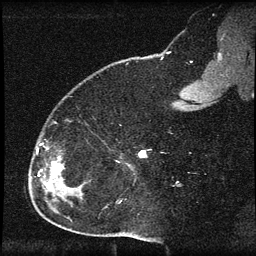
Breast MRI (dynamic contrast-enhanced), one sagittal slice; slice 19 of 60 in the series (ordered by position); dynamic contrast-enhanced series, image 2 of 3 at this slice position (ordered by acquisition); 1.5 T; TE 4.2 ms, TR 8.2 ms; 2 mm slice thickness; 256 × 256 image matrix, field of view 180 × 180 mm. Patient: female, 32 years.
Structures marked on this image (semi-automatic segmentation, software-assisted and operator-edited):
- analysis volume of interest (the breast-tissue region the enhancement analysis was run in; not a lesion): box from (x=31, y=139) to (x=65, y=184) px
- tumour enhancement mask (voxels above the 70 % enhancement threshold inside the analysis volume of interest): (x=47, y=162)–(x=56, y=184)